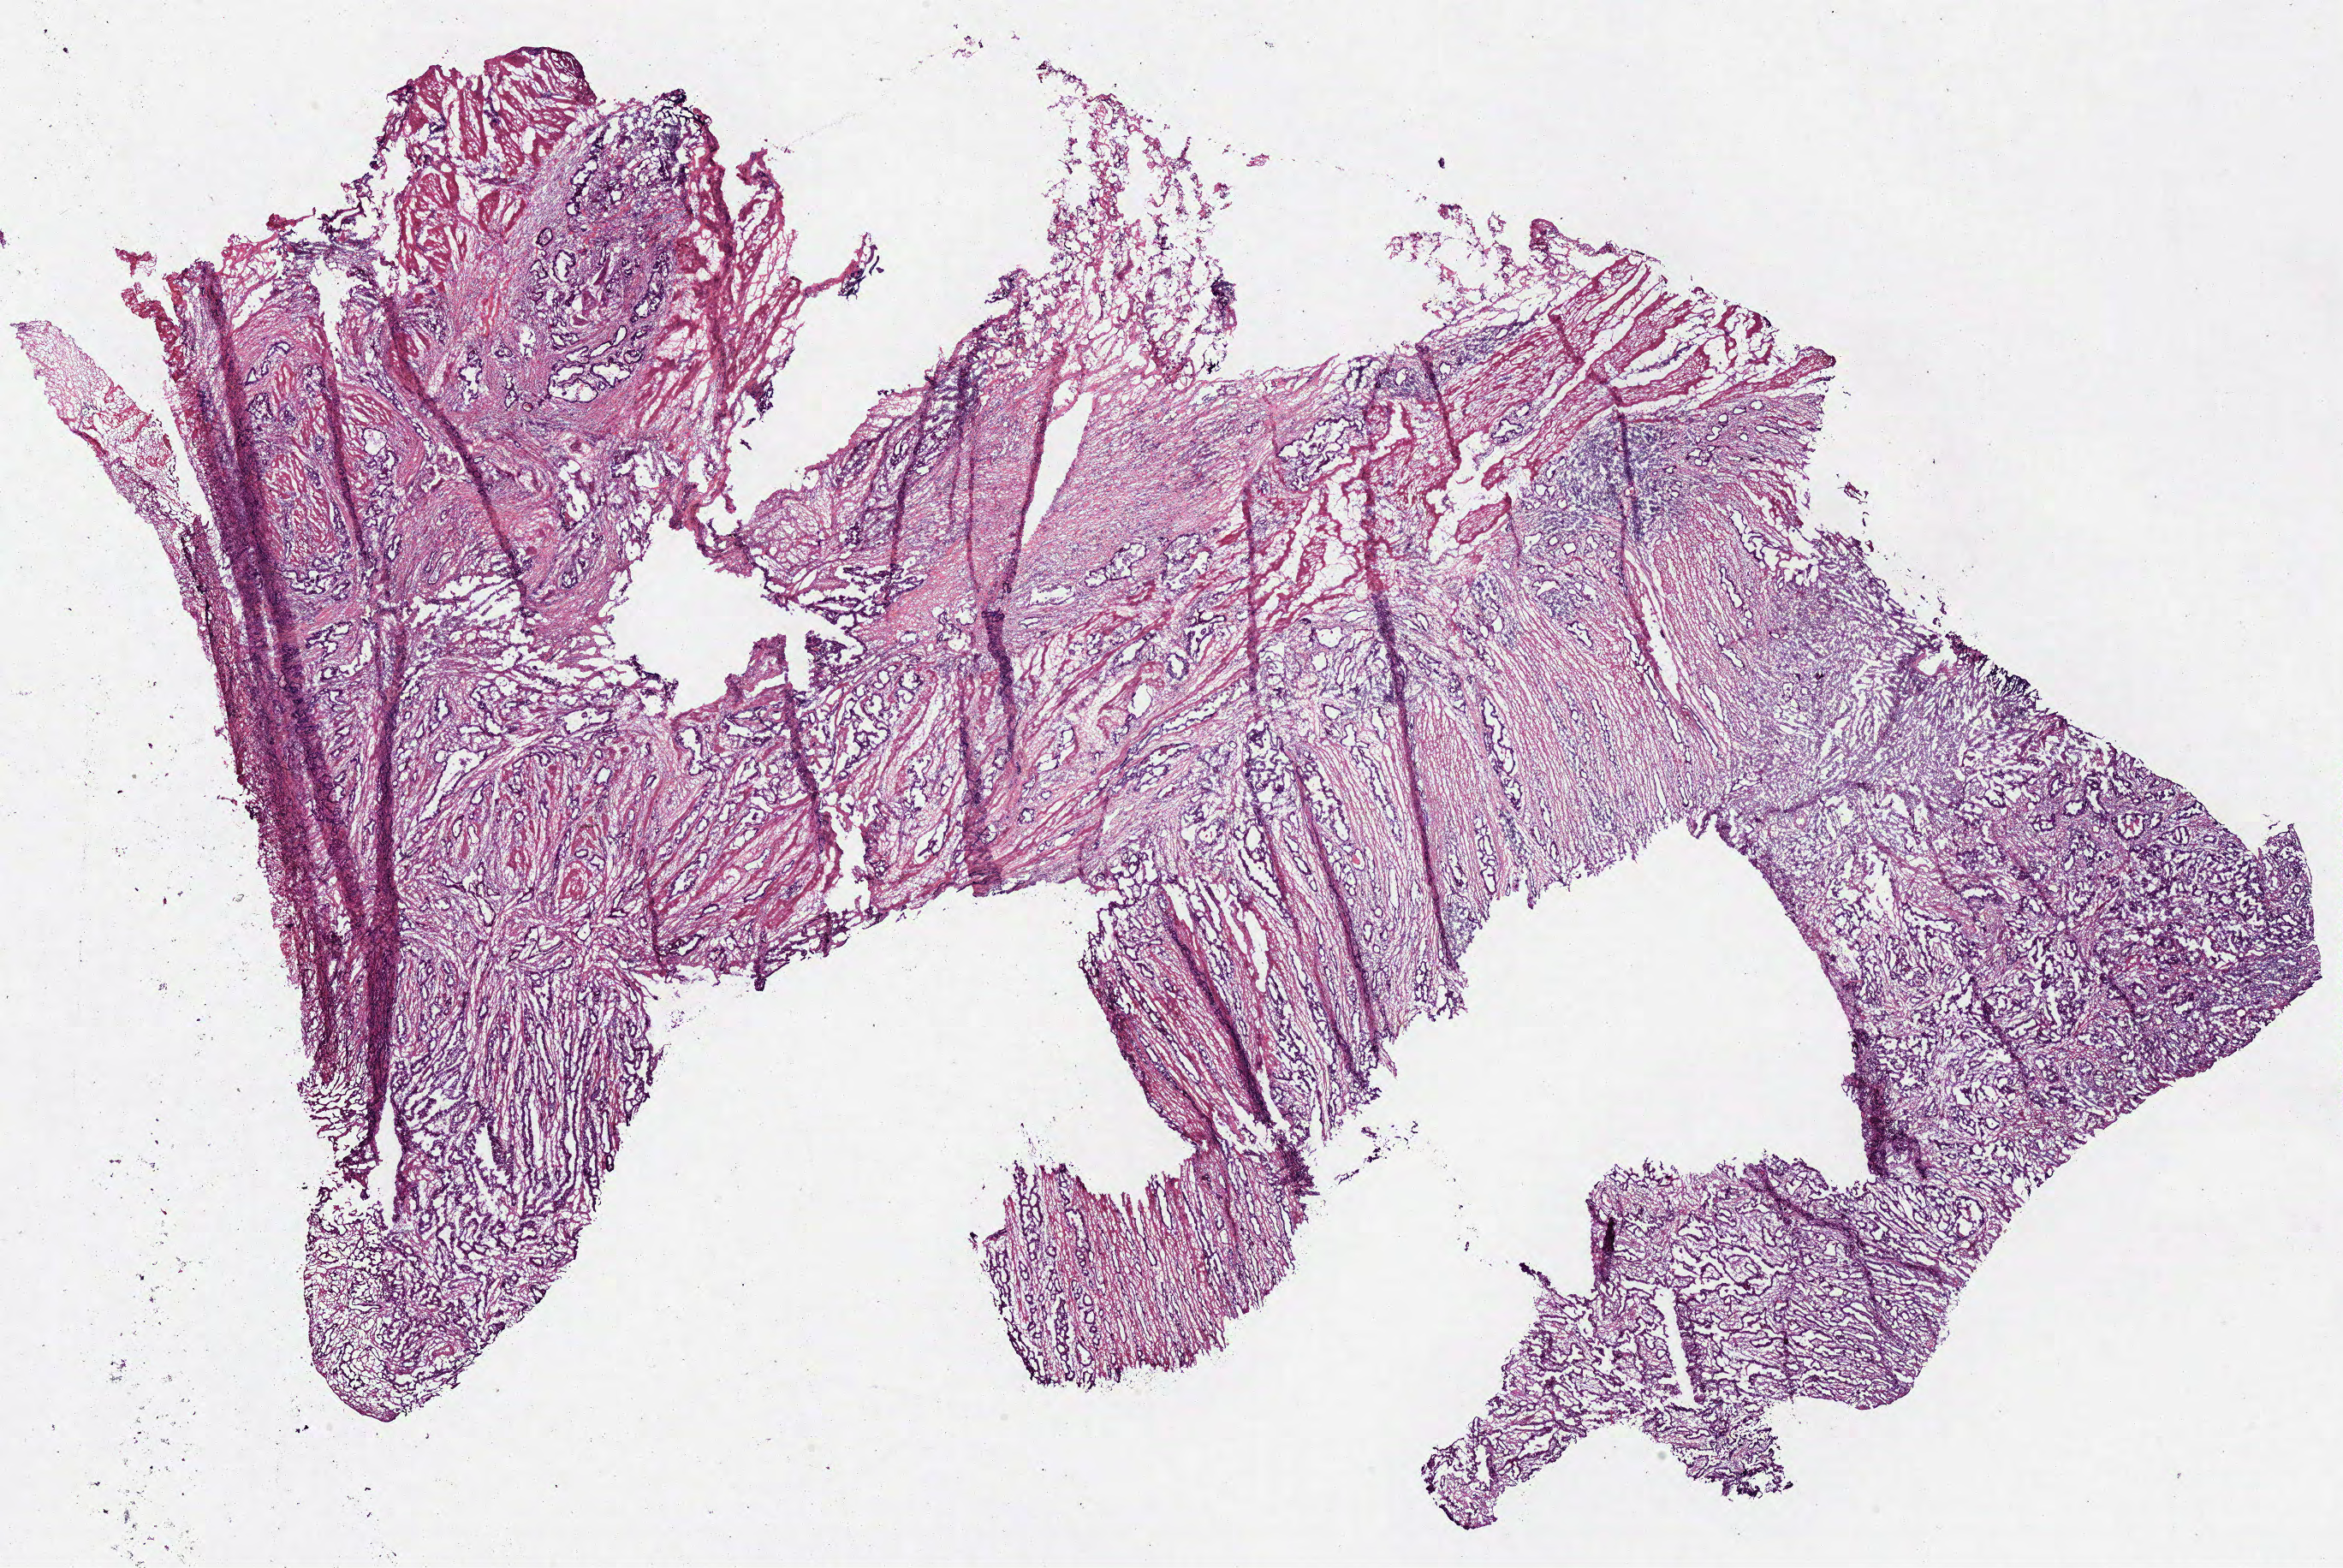
Digitized H&E tissue section (whole slide), low-resolution overview of the scanned area, about 21.6 x 14.4 mm; frozen section from the bottom of the tissue portion; rectum, primary tumour sample. Male, age 67 years at initial diagnosis. Slide review estimates, as recorded: tumour cells 99%, tumour nuclei 70%, necrosis 1%. Infiltration values recorded for this section: lymphocyte infiltration 15%.
• lymph nodes positive (case pathology): 0 of 1 examined
• diagnosis: Adenocarcinoma, NOS (connective, subcutaneous and other soft tissues of abdomen)
• AJCC pathologic stage: IIA (7th edition)